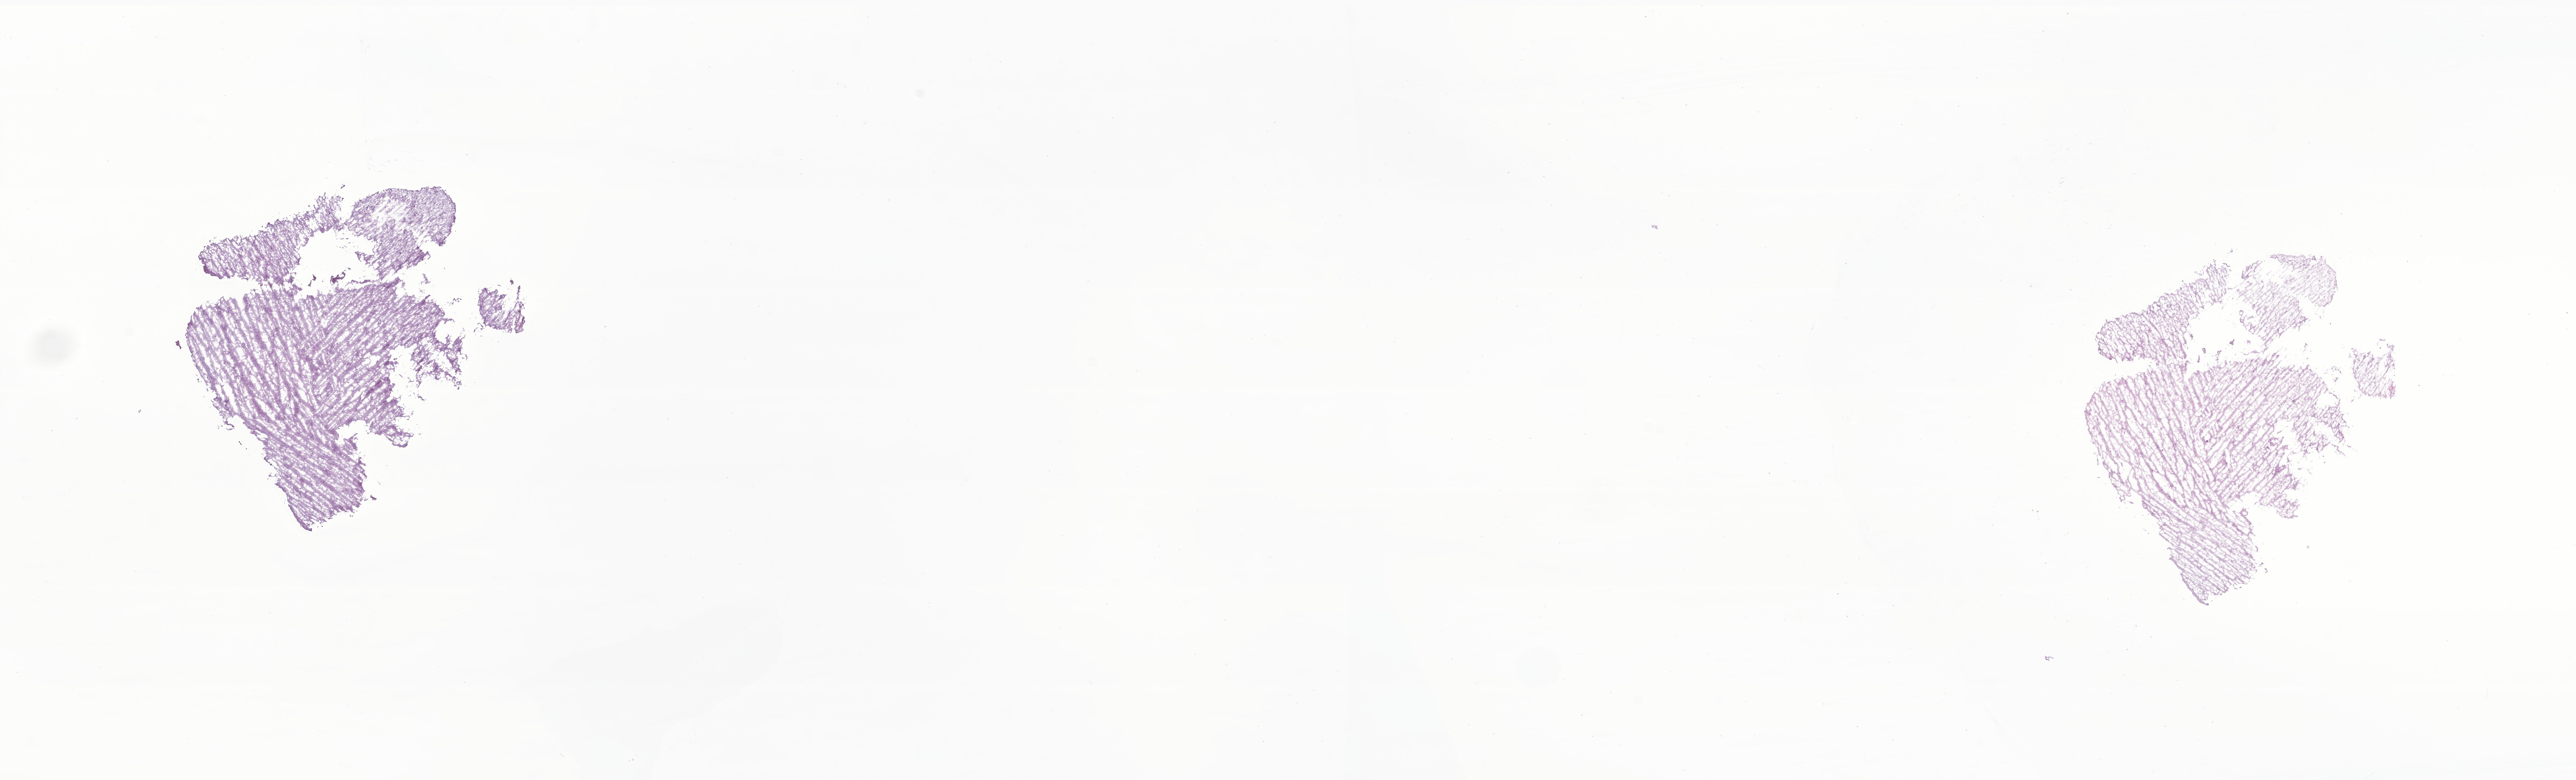
Digitized H&E-stained section of tumor tissue from the brain — low-resolution overview of the scanned area, about 27.7 x 8.4 mm. Frozen section. Female patient, age 200 months.
Recorded diagnosis: Pilocytic astrocytoma.